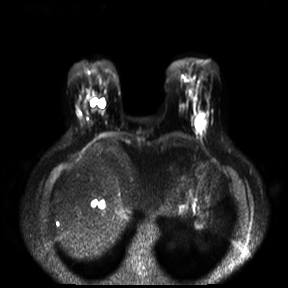
Breast MRI, one axial slice. Position 6 of 30 along the scan axis. Diffusion-weighted series; image 2 of 4 stored at this slice position (different b-values; order by instance number). 3 T. 4 mm slice thickness. 288 × 288 image matrix, field of view 360 × 360 mm. Female patient.
Annotated regions visible in this slice (outlined manually by an expert reader):
- tumour on diffusion-weighted imaging: bounding box [x1, y1, x2, y2] px = [195, 115, 205, 129]